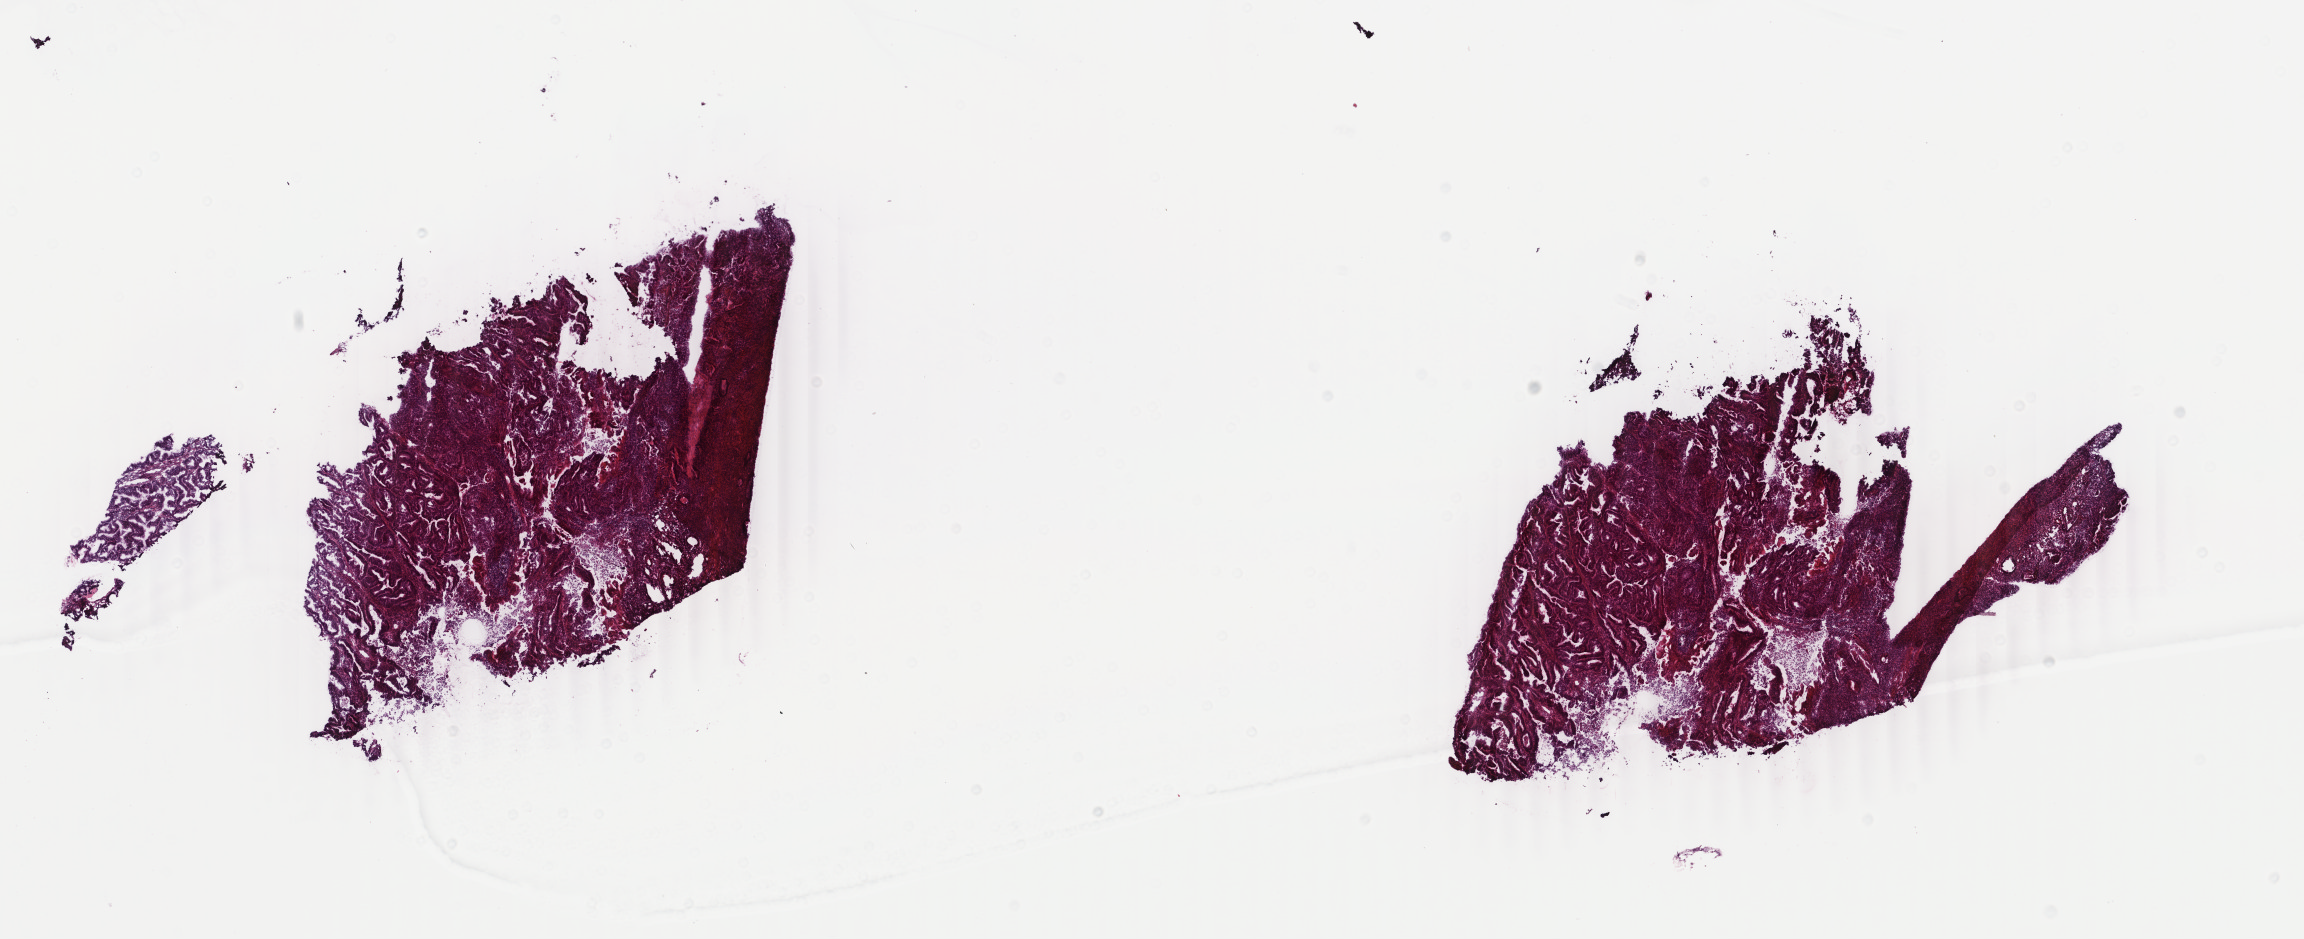
Digitized Hematoxylin and eosin (H&E) stained tissue section (whole slide) — a low-resolution overview of the entire scanned area, about 18.3 x 7.5 mm (acquisition: 40x scan); frozen section; primary tumour sample from the uterus. Female, age 60 years at initial diagnosis. Histologic grade: G1 (well differentiated). Composition of this section per pathologist review: tumour cells 70%, tumour nuclei 70%, normal cells 10%, stromal cells 15%, necrosis 5%. Infiltration values recorded for this section: lymphocyte infiltration 50%, monocyte infiltration 20%, neutrophil infiltration 20%.
- histologic diagnosis: Endometrioid adenocarcinoma, NOS (endometrium)
- FIGO stage: IA